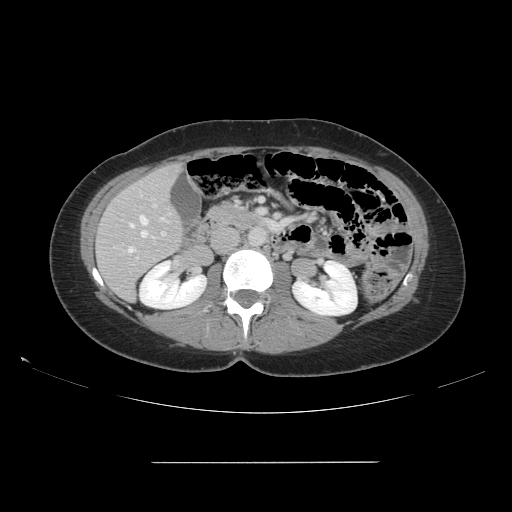
Contrast-enhanced abdominal CT, one axial slice. Slice 65 of 151 in the series (ordered by position). Intravenous contrast given. Soft-tissue window (W 400 / L 40 HU). 512 × 512 image matrix, field of view 421 × 421 mm. Female patient, age 46 years. Case-level facts recorded for this patient, not image findings: diagnosis: colorectal cancer liver metastases, imaged before liver resection; multiple liver metastases: yes; largest metastasis: 3 cm; chemotherapy before resection: no.
Structures marked on this image (outlined manually by an expert reader):
- hepatic veins: bounding box (x1, y1, x2, y2) in pixels: (127, 215, 164, 253)
- liver: (97, 165, 183, 300)
- planned liver remnant (the part of the liver to remain after resection): (97, 165, 183, 300)
- portal vein (with intrahepatic branches): (136, 203, 166, 260)